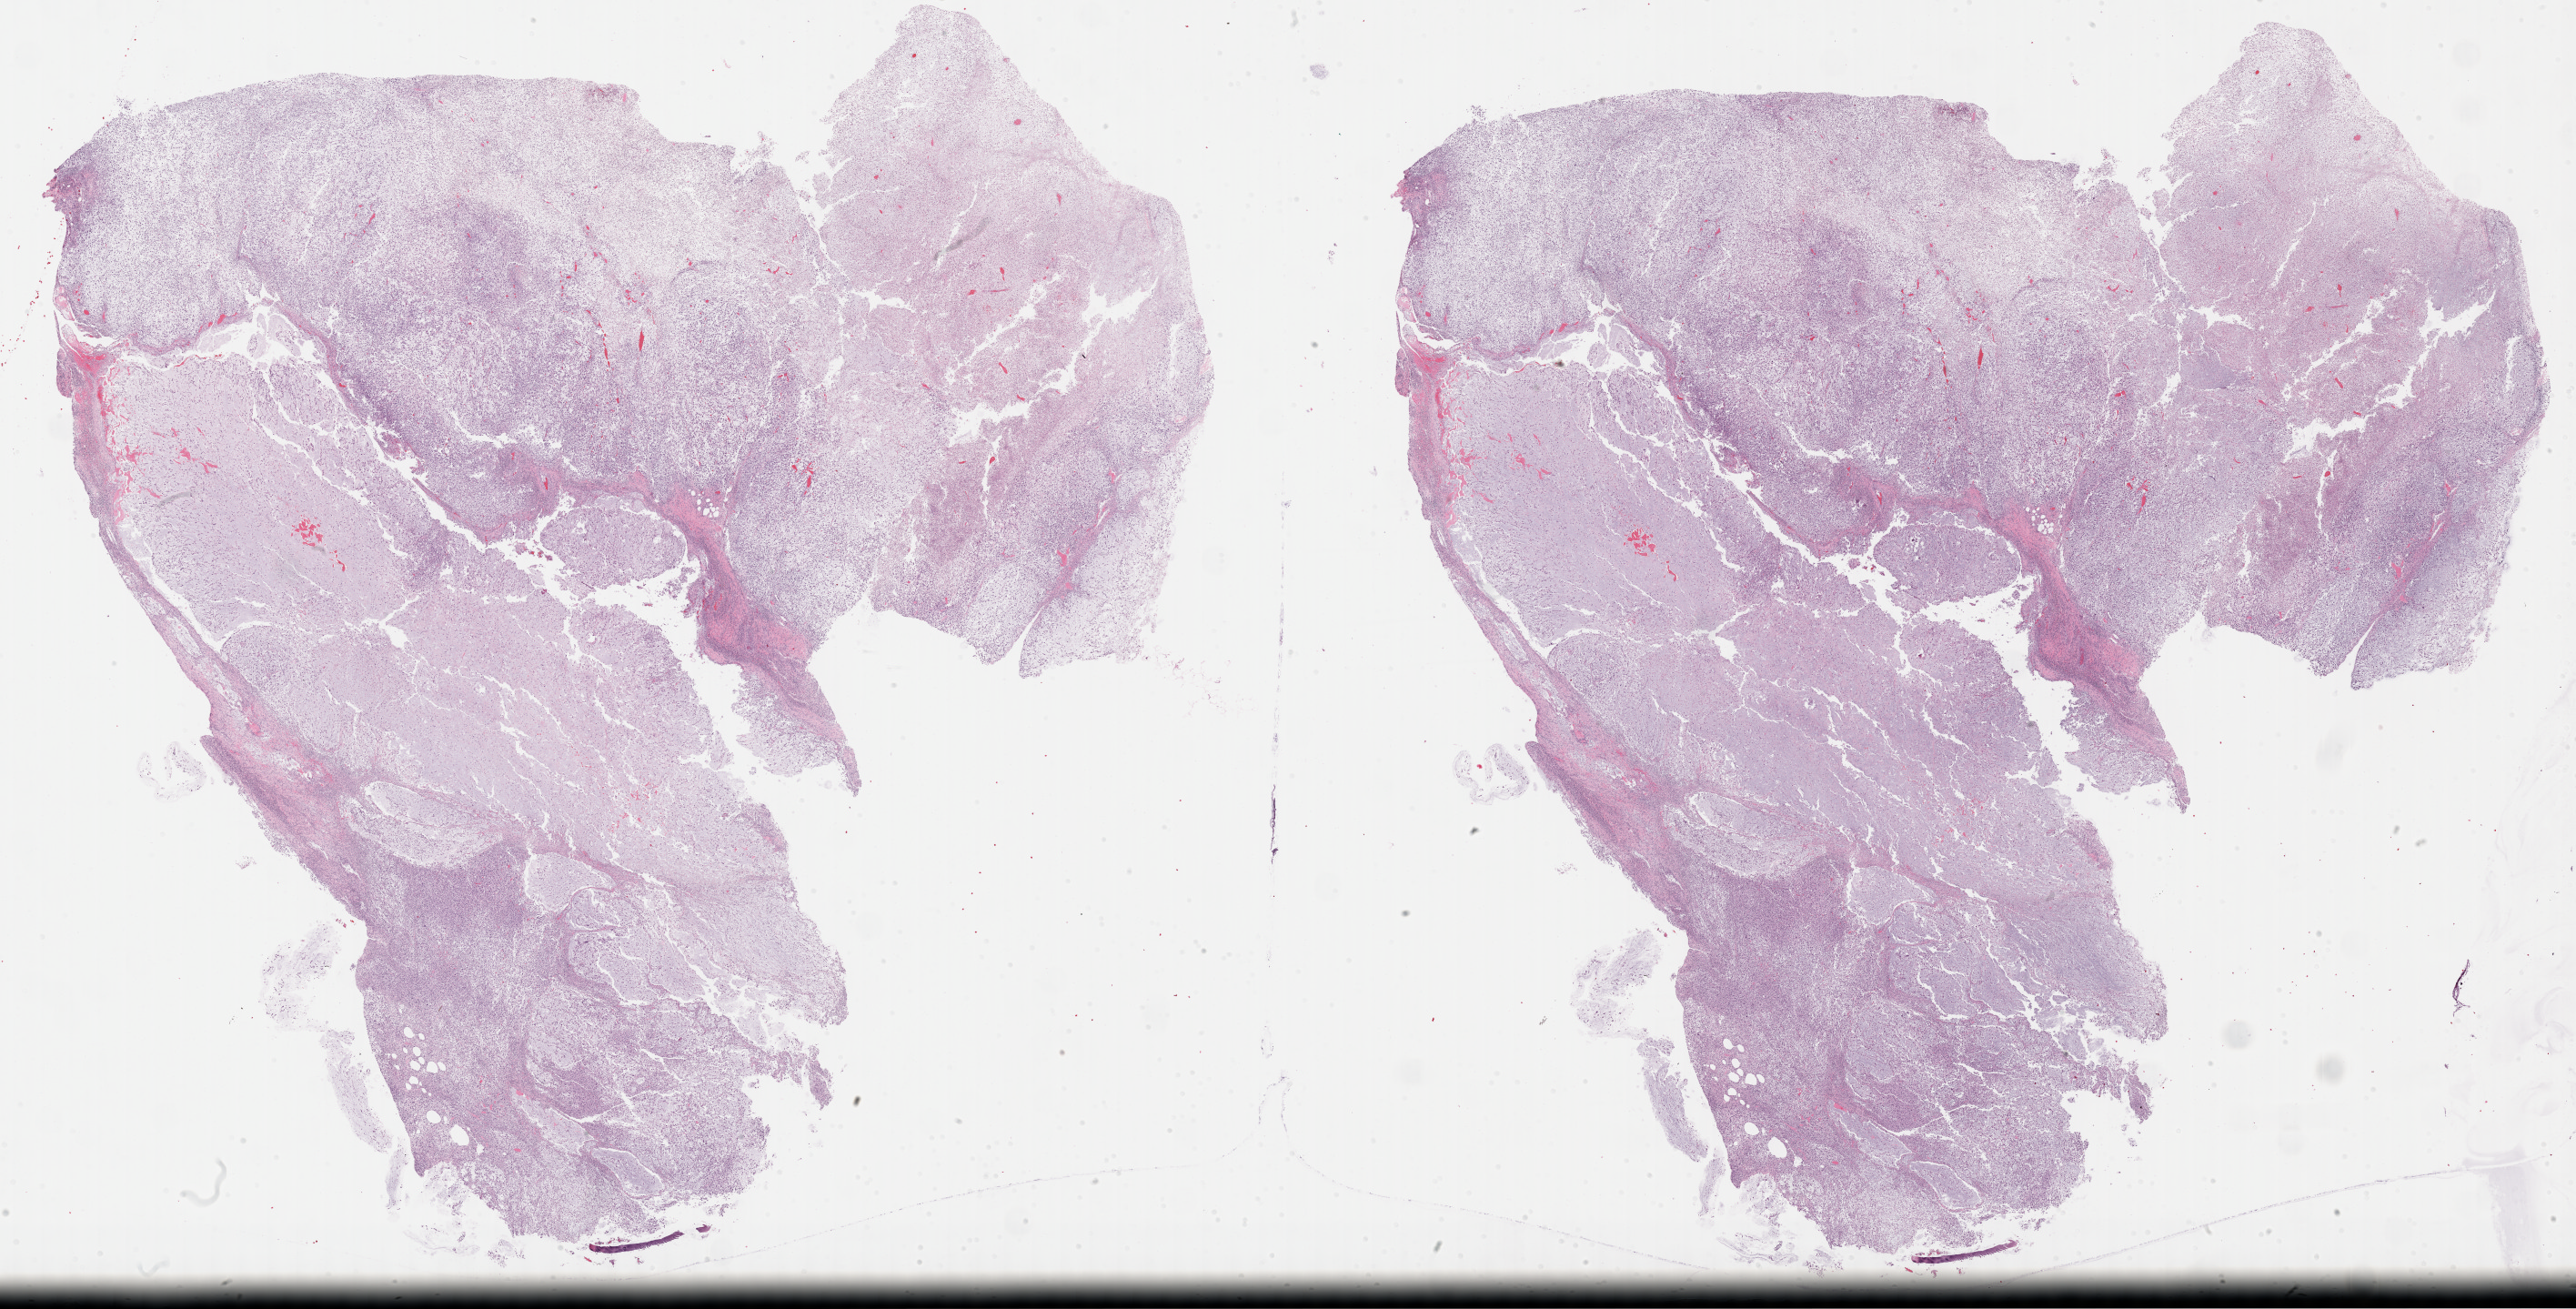
Hematoxylin and eosin (H&E) stained whole-slide image — low-resolution overview of the scanned area, about 45.8 x 23.3 mm (from a 40x scan); FFPE section; primary tumour sample from the connective, subcutaneous and other soft tissues. Male patient; age at initial diagnosis 60 years.
Histologic diagnosis: Fibromyxosarcoma (connective, subcutaneous and other soft tissues of thorax).